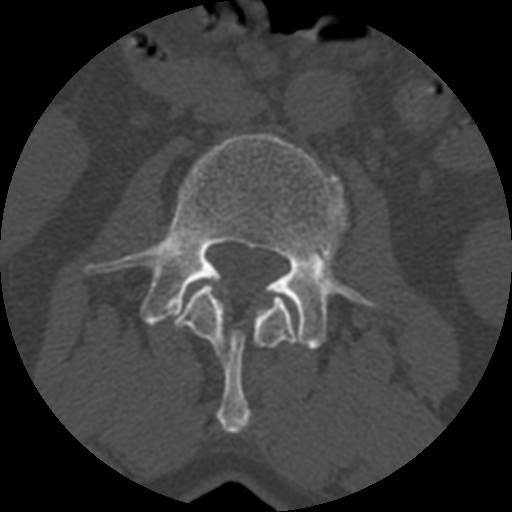
CT including the spine, one axial slice. Slice 316 of 399 in the series (ordered by position). Reconstruction kernel STANDARD. Bone window (W 1800 / L 400 HU). 1.25 mm slice thickness. 512 × 512 image matrix, field of view 160 × 160 mm. Patient age 71 years. From the clinical record (not read from this slice): primary cancer: prostate.
Annotated regions visible in this slice (semi-automatically segmented with operator editing):
- L2 vertebra: box from (x=174, y=284) to (x=295, y=433) px
- L3 vertebra: (x=83, y=132)–(x=400, y=350)